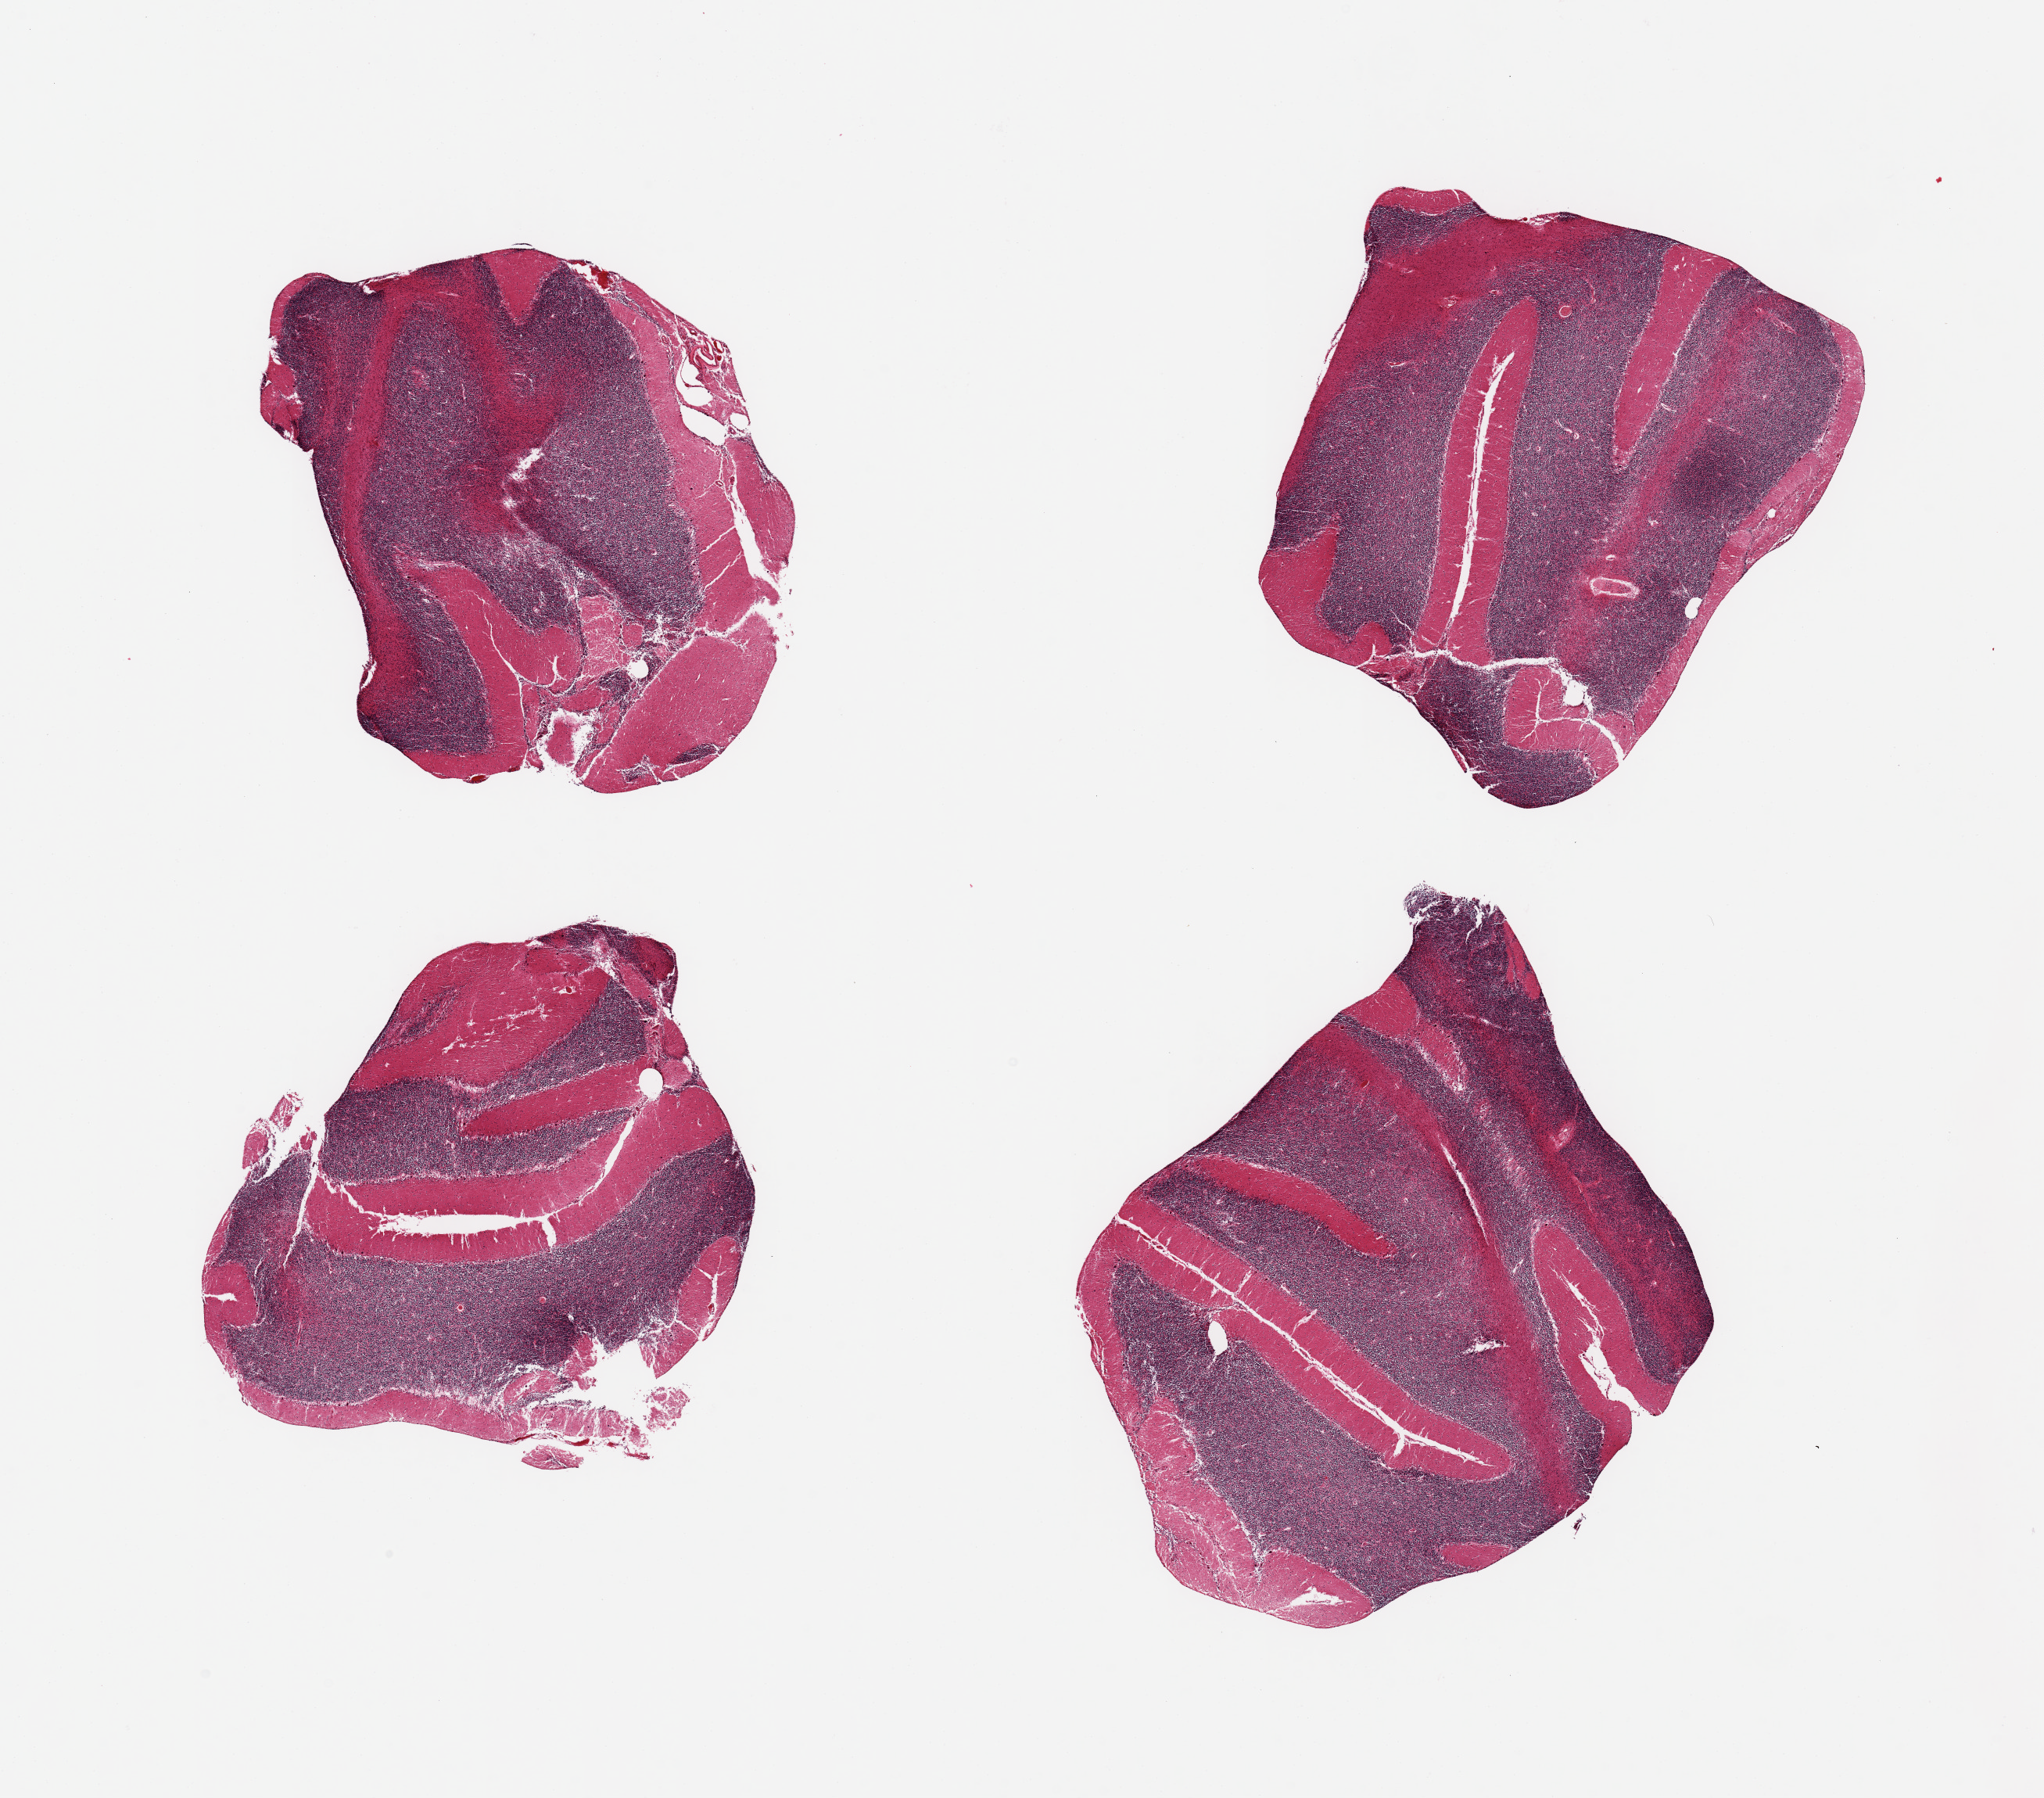
H&E whole-slide image — low-resolution overview of the scanned area, about 20.7 x 18.2 mm. PAXgene-fixed, paraffin-embedded tissue. Target tissue: cerebellum. Donor tissue sample.
Reviewer comment on this tissue sample: 4 pieces, no abnormalities.